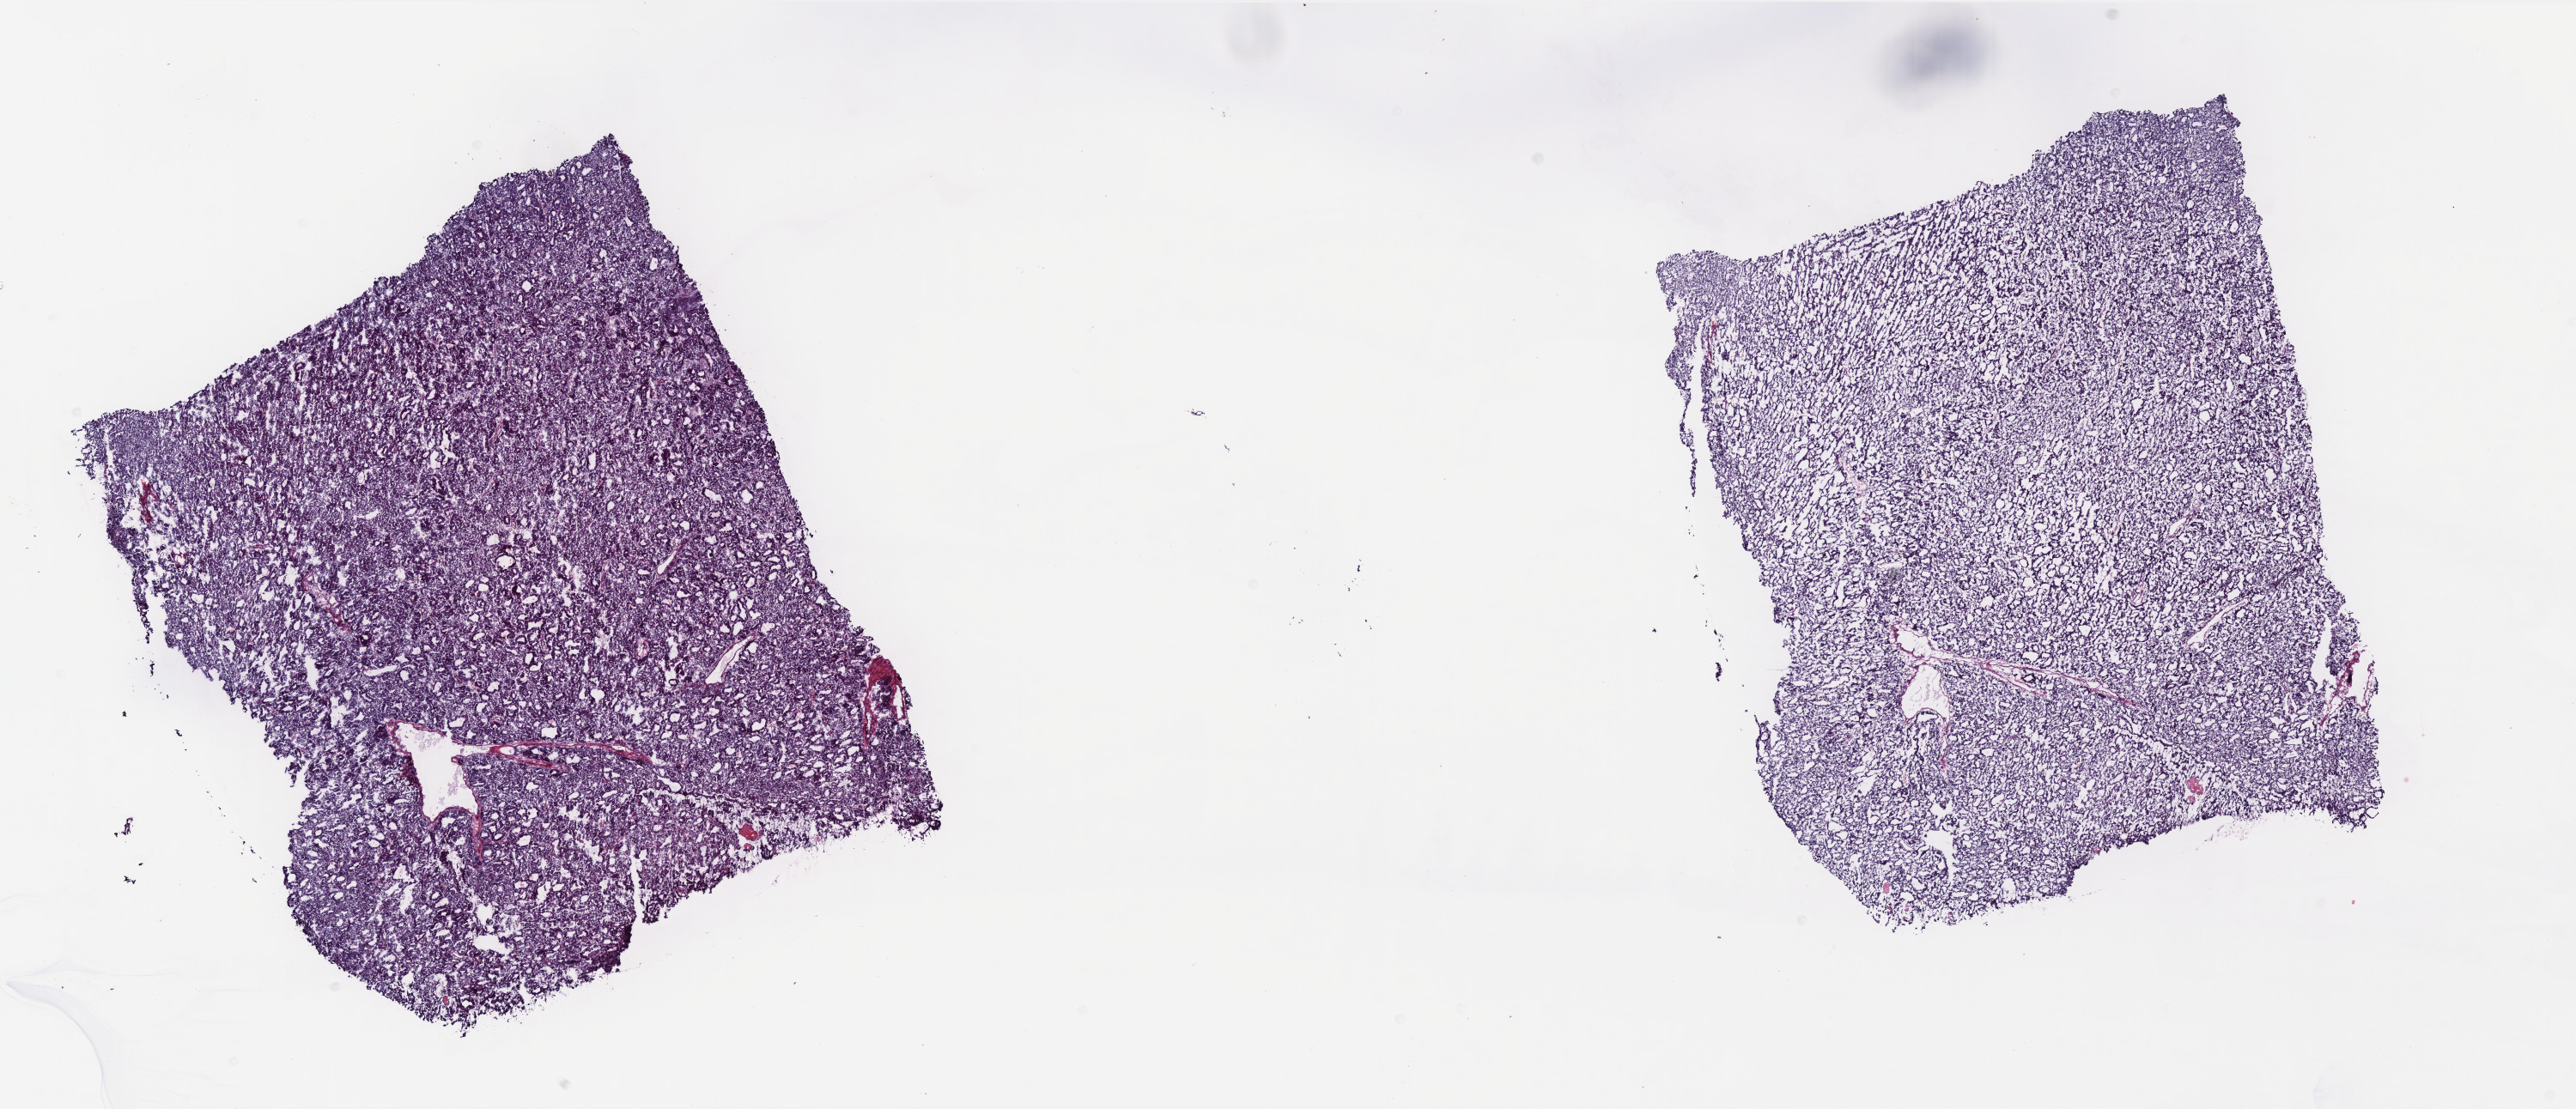
Digitized Hematoxylin and eosin (H&E) stained tissue section (whole slide), shown as a low-resolution overview of the whole scanned area (about 24.1 x 10.4 mm), frozen section, primary tumour sample from the uterus. Patient: female, age at initial diagnosis 74 years. Histologic grade: G2 (moderately differentiated). Composition of this section per pathologist review: tumour cells 100%, tumour nuclei 90%, normal cells 0%, stromal cells 0%, necrosis 0%. Infiltration values recorded for this section: lymphocyte infiltration 0%, monocyte infiltration 0%, neutrophil infiltration 0%.
* FIGO stage: IB
* histologic diagnosis: Endometrioid adenocarcinoma, NOS (endometrium)
* lymph nodes positive (case pathology): 0 of 12 examined